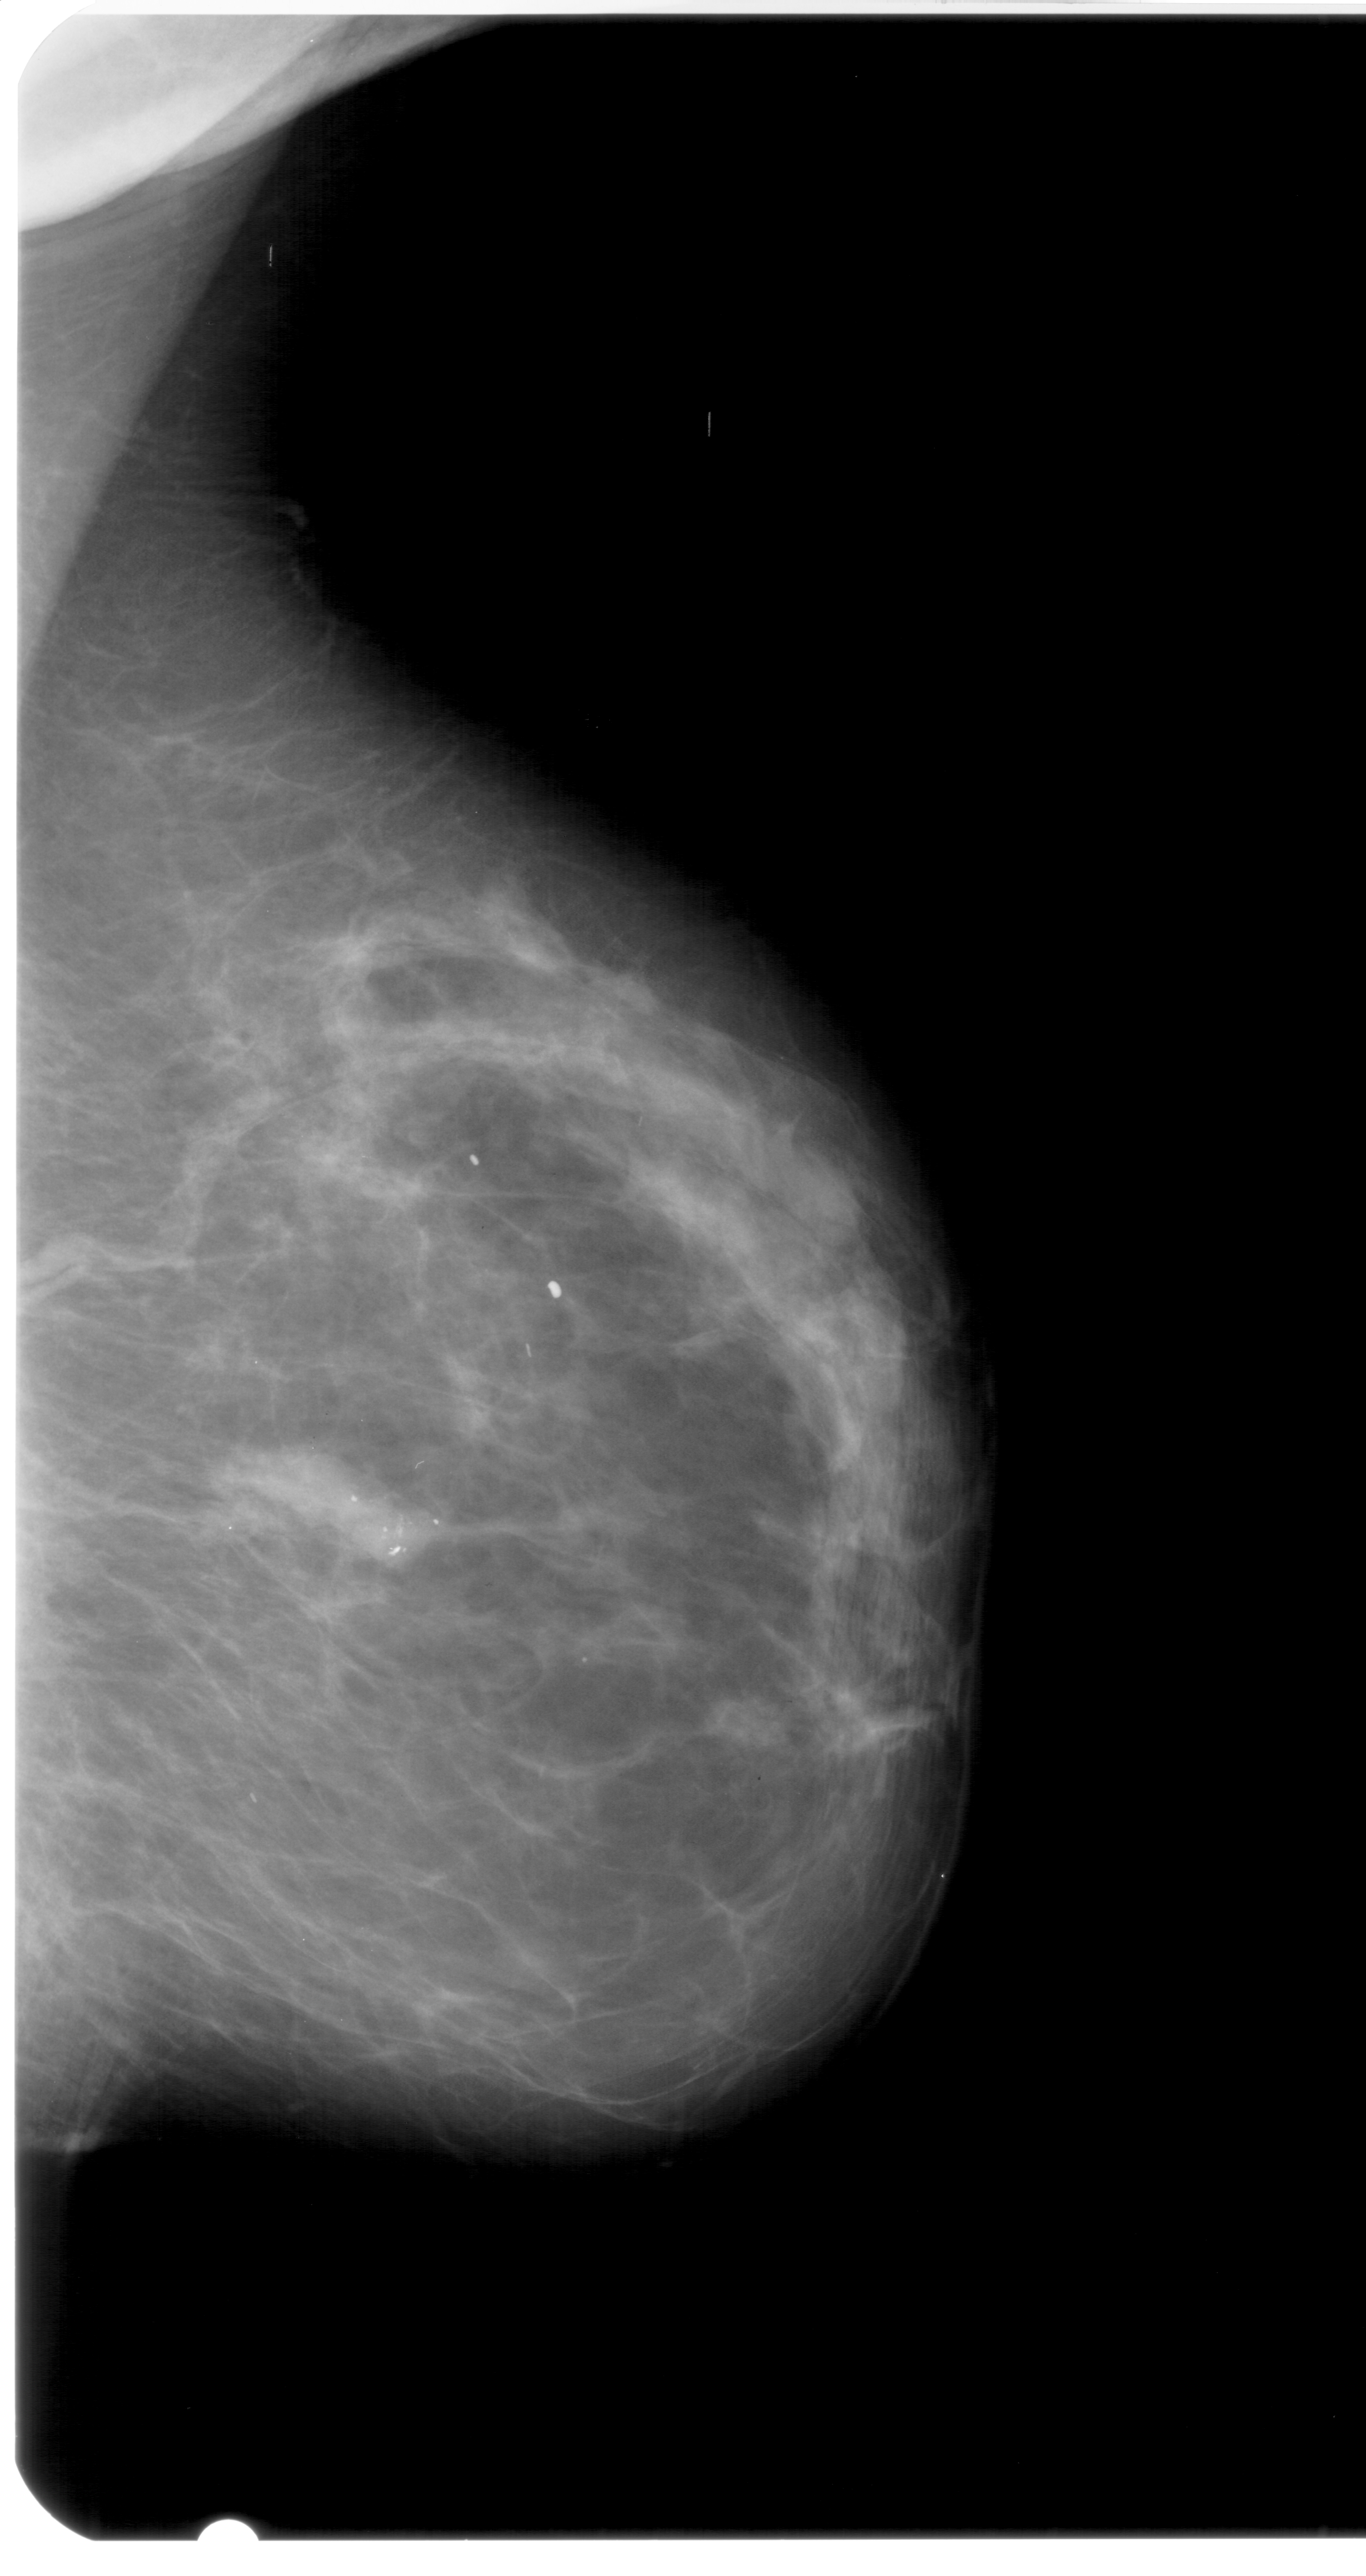
Mammogram (digitized film). Right breast. MLO view. 1366 × 2576 image matrix.
Expert-marked regions of interest on this image (one box per marked abnormality):
- calcifications, morphology pleomorphic, distribution clustered; BI-RADS assessment category 4; subtlety rating 5 on a 1 (subtle) to 5 (obvious) scale; pathology (as recorded): malignant: bounding box <347,1484,472,1579> (left, top, right, bottom; pixels)